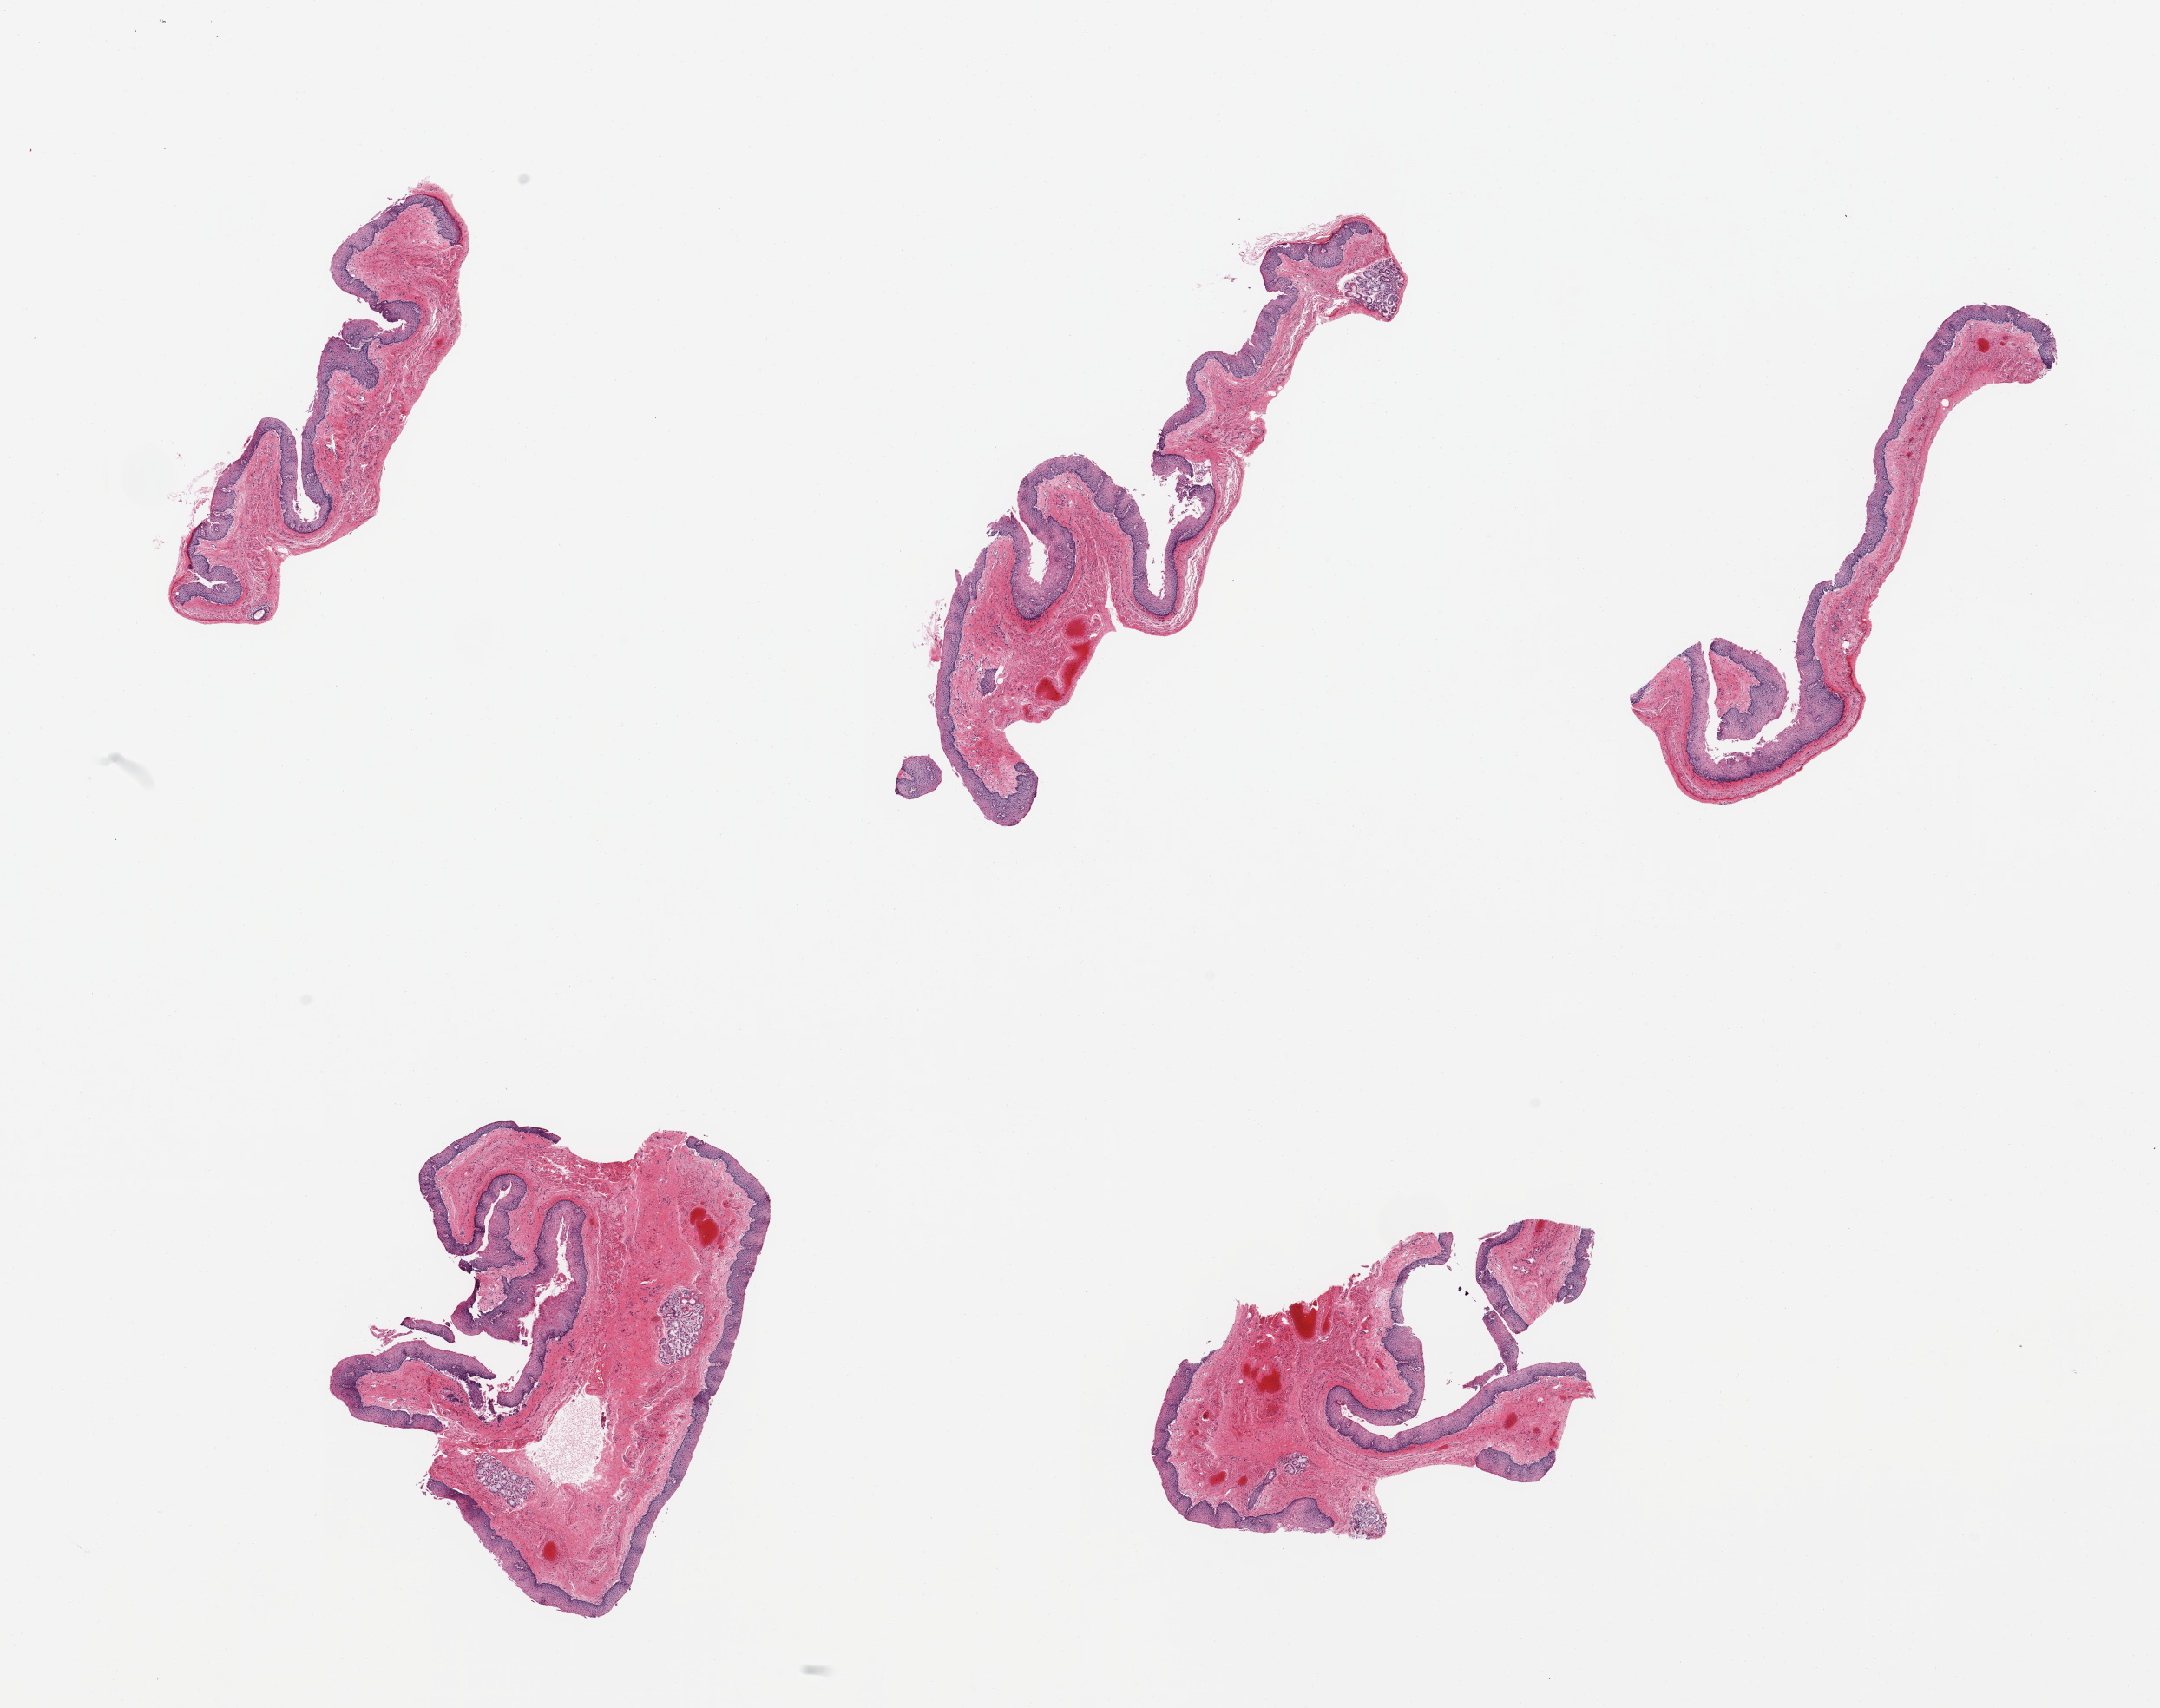
Digitized hematoxylin and eosin (H&E)-stained section, low-resolution overview of the scanned area, about 19.7 x 15.6 mm (acquisition: 20x scan), PAXgene-fixed paraffin-embedded (PFPE) section, target tissue: esophageal mucous membrane, donor tissue sample. Donor sex: male.
• pathologist's review note for this sample: 5 pieces, squamous mucosa up to ~0.2mm, ~10-30% thickness